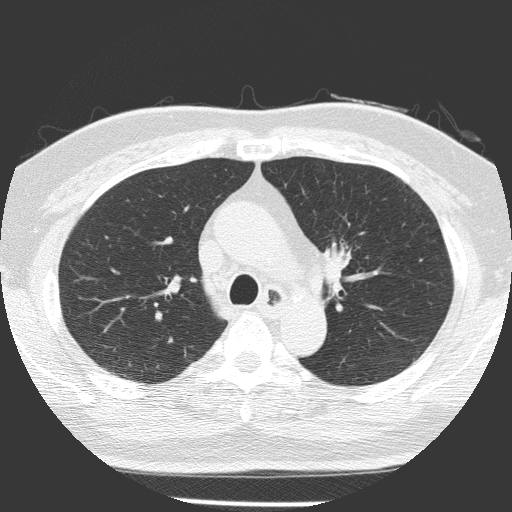
Low-dose screening chest CT, one axial slice; slice 106 of 156 in the series (ordered by position); reconstruction kernel FC51; 120 kVp; lung window (W 1500 / L -600 HU); 2 mm slice thickness; 512 × 512 image matrix, field of view 309 × 309 mm.
Structures marked on this image (manually delineated by an expert):
- lesion 1 (tumor, upper lobe of left lung): box from (x=324, y=245) to (x=351, y=270) px